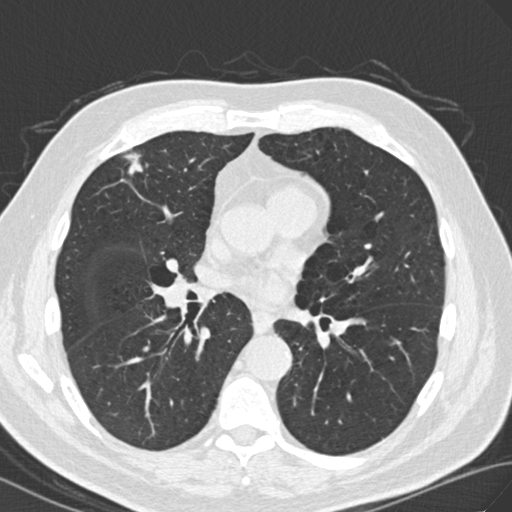
Low-dose screening chest CT, axial slice, second screening round (one year after baseline), lung window (W 1500 / L -600 HU), 2 mm slice thickness, standard (soft-tissue) reconstruction kernel (B30f), slice 87 of 171 in the series. Male participant, aged 69 years at enrolment. Current smoker at enrolment.
Lesion marked by an expert reader, bounding box (x1, y1, x2, y2) in pixels: (108, 140, 162, 192). The screening reader recorded 3 non-calcified nodules or masses ≥4 mm on this exam (right upper lobe, right lower lobe, right lower lobe); which of them this box marks is not recorded. Official screen result: positive, other. Later outcome: lung cancer diagnosed 183 days after this screen — adenocarcinoma, NOS, right upper lobe, moderately differentiated (G2), stage IIA (AJCC 6th edition), 20 mm at pathology.